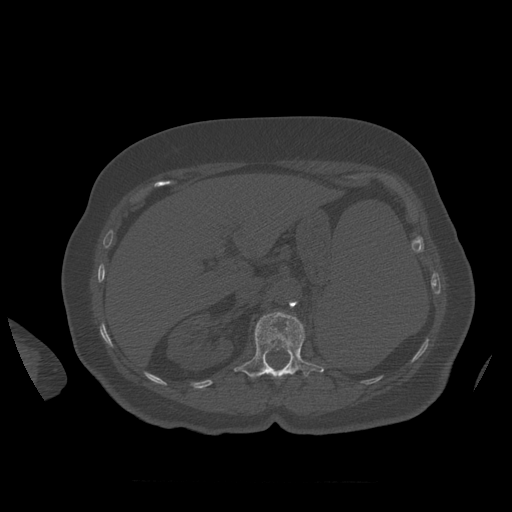
CT including the spine, one axial slice. Position 280 of 399 along the scan axis. 120 kVp. Bone window (W 1800 / L 400 HU). 1.25 mm slice thickness. 512 × 512 image matrix, field of view 404 × 404 mm. Patient age 81 years. Case-level facts recorded for this patient, not image findings: primary cancer: renal.
Annotated regions visible in this slice (semi-automatic segmentation, software-assisted and operator-edited):
- L1 vertebra: bounding box [x1, y1, x2, y2] px = [234, 312, 325, 379]